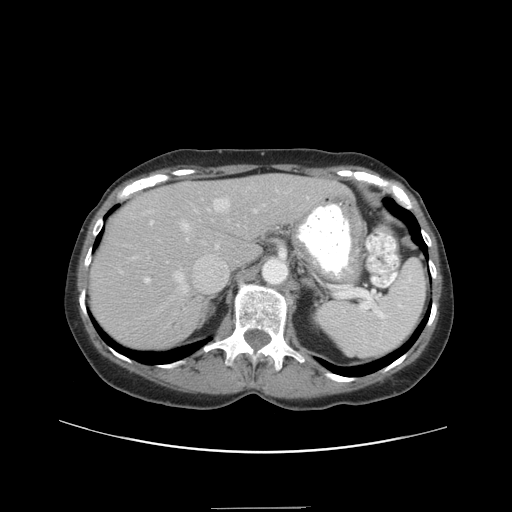
Contrast-enhanced abdominal CT, one axial slice; slice 27 of 38 in the series (ordered by position); reconstruction kernel STANDARD; intravenous contrast given; soft-tissue window (W 400 / L 40 HU); 5 mm slice thickness; 512 × 512 image matrix, field of view 388 × 388 mm. Female patient, age 64 years. From the clinical record (not read from this slice): diagnosis: colorectal cancer liver metastases, imaged before liver resection; multiple liver metastases: no; largest metastasis: 3.8 cm; chemotherapy before resection: yes.
Annotated regions visible in this slice (expert manual segmentation):
- hepatic veins: box from (x=173, y=199) to (x=230, y=294) px
- liver: (x=93, y=176)–(x=340, y=350)
- planned liver remnant (the part of the liver to remain after resection): (x=139, y=176)–(x=342, y=267)
- portal vein (with intrahepatic branches): (x=144, y=205)–(x=265, y=283)